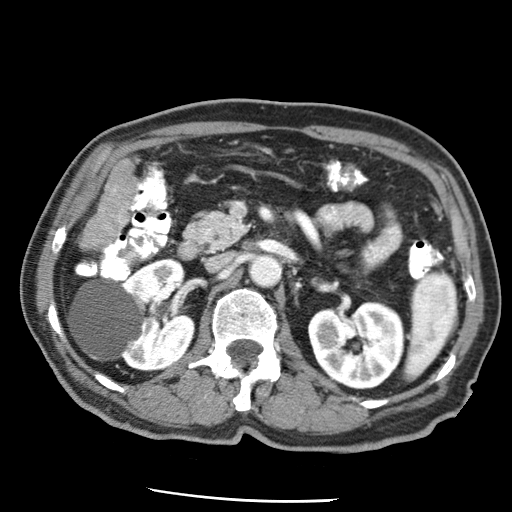
Contrast-enhanced abdominal CT (liver protocol), one axial slice. Slice 11 of 79 in the series (ordered by position). Soft-tissue window (W 400 / L 40 HU). 2.5 mm slice thickness. 512 × 512 image matrix. From the clinical record (not read from this slice): diagnosis: hepatocellular carcinoma (patient treated with transarterial chemoembolisation; whether this scan precedes or follows treatment is not stated here); TNM stage (as recorded): Stage-IIIA; Child-Pugh class: A; tumour nodularity: multinodular.
Annotated regions visible in this slice (semi-automatically segmented with operator editing):
- liver parenchyma outside the tumour (the mass and vessels are separate outlines, so this box may not span the whole liver): bounding box (x1, y1, x2, y2) in pixels: (85, 159, 134, 246)
- liver vessels: (114, 189, 125, 223)